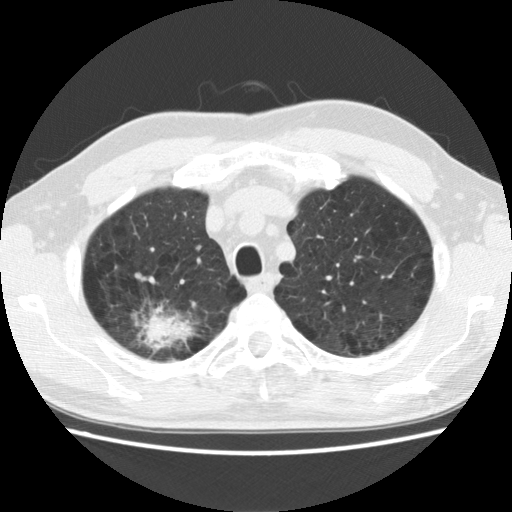
Low-dose screening chest CT, axial slice, first (baseline) screen, lung window (W 1500 / L -600 HU), 2.5 mm slice thickness. Male, age 64 years at enrolment.
Expert-annotated lung lesion, box from (x=113, y=293) to (x=202, y=365) px. The exam's reader record, not a measurement of the box and not confirmed to be the same lesion: non-calcified nodule or mass ≥4 mm, right upper lobe, 39 × 31 mm, spiculated (stellate) margins, mixed attenuation. Official screen result: positive, change unspecified: nodule(s) >= 4 mm or enlarging nodule(s), mass(es), or other non-specific abnormalities suspicious for lung cancer. Participant outcome: lung cancer diagnosed 74 days after this screen — adenocarcinoma, NOS, right upper lobe, moderately differentiated (G2), stage IB (AJCC 6th edition), 40 mm at pathology.